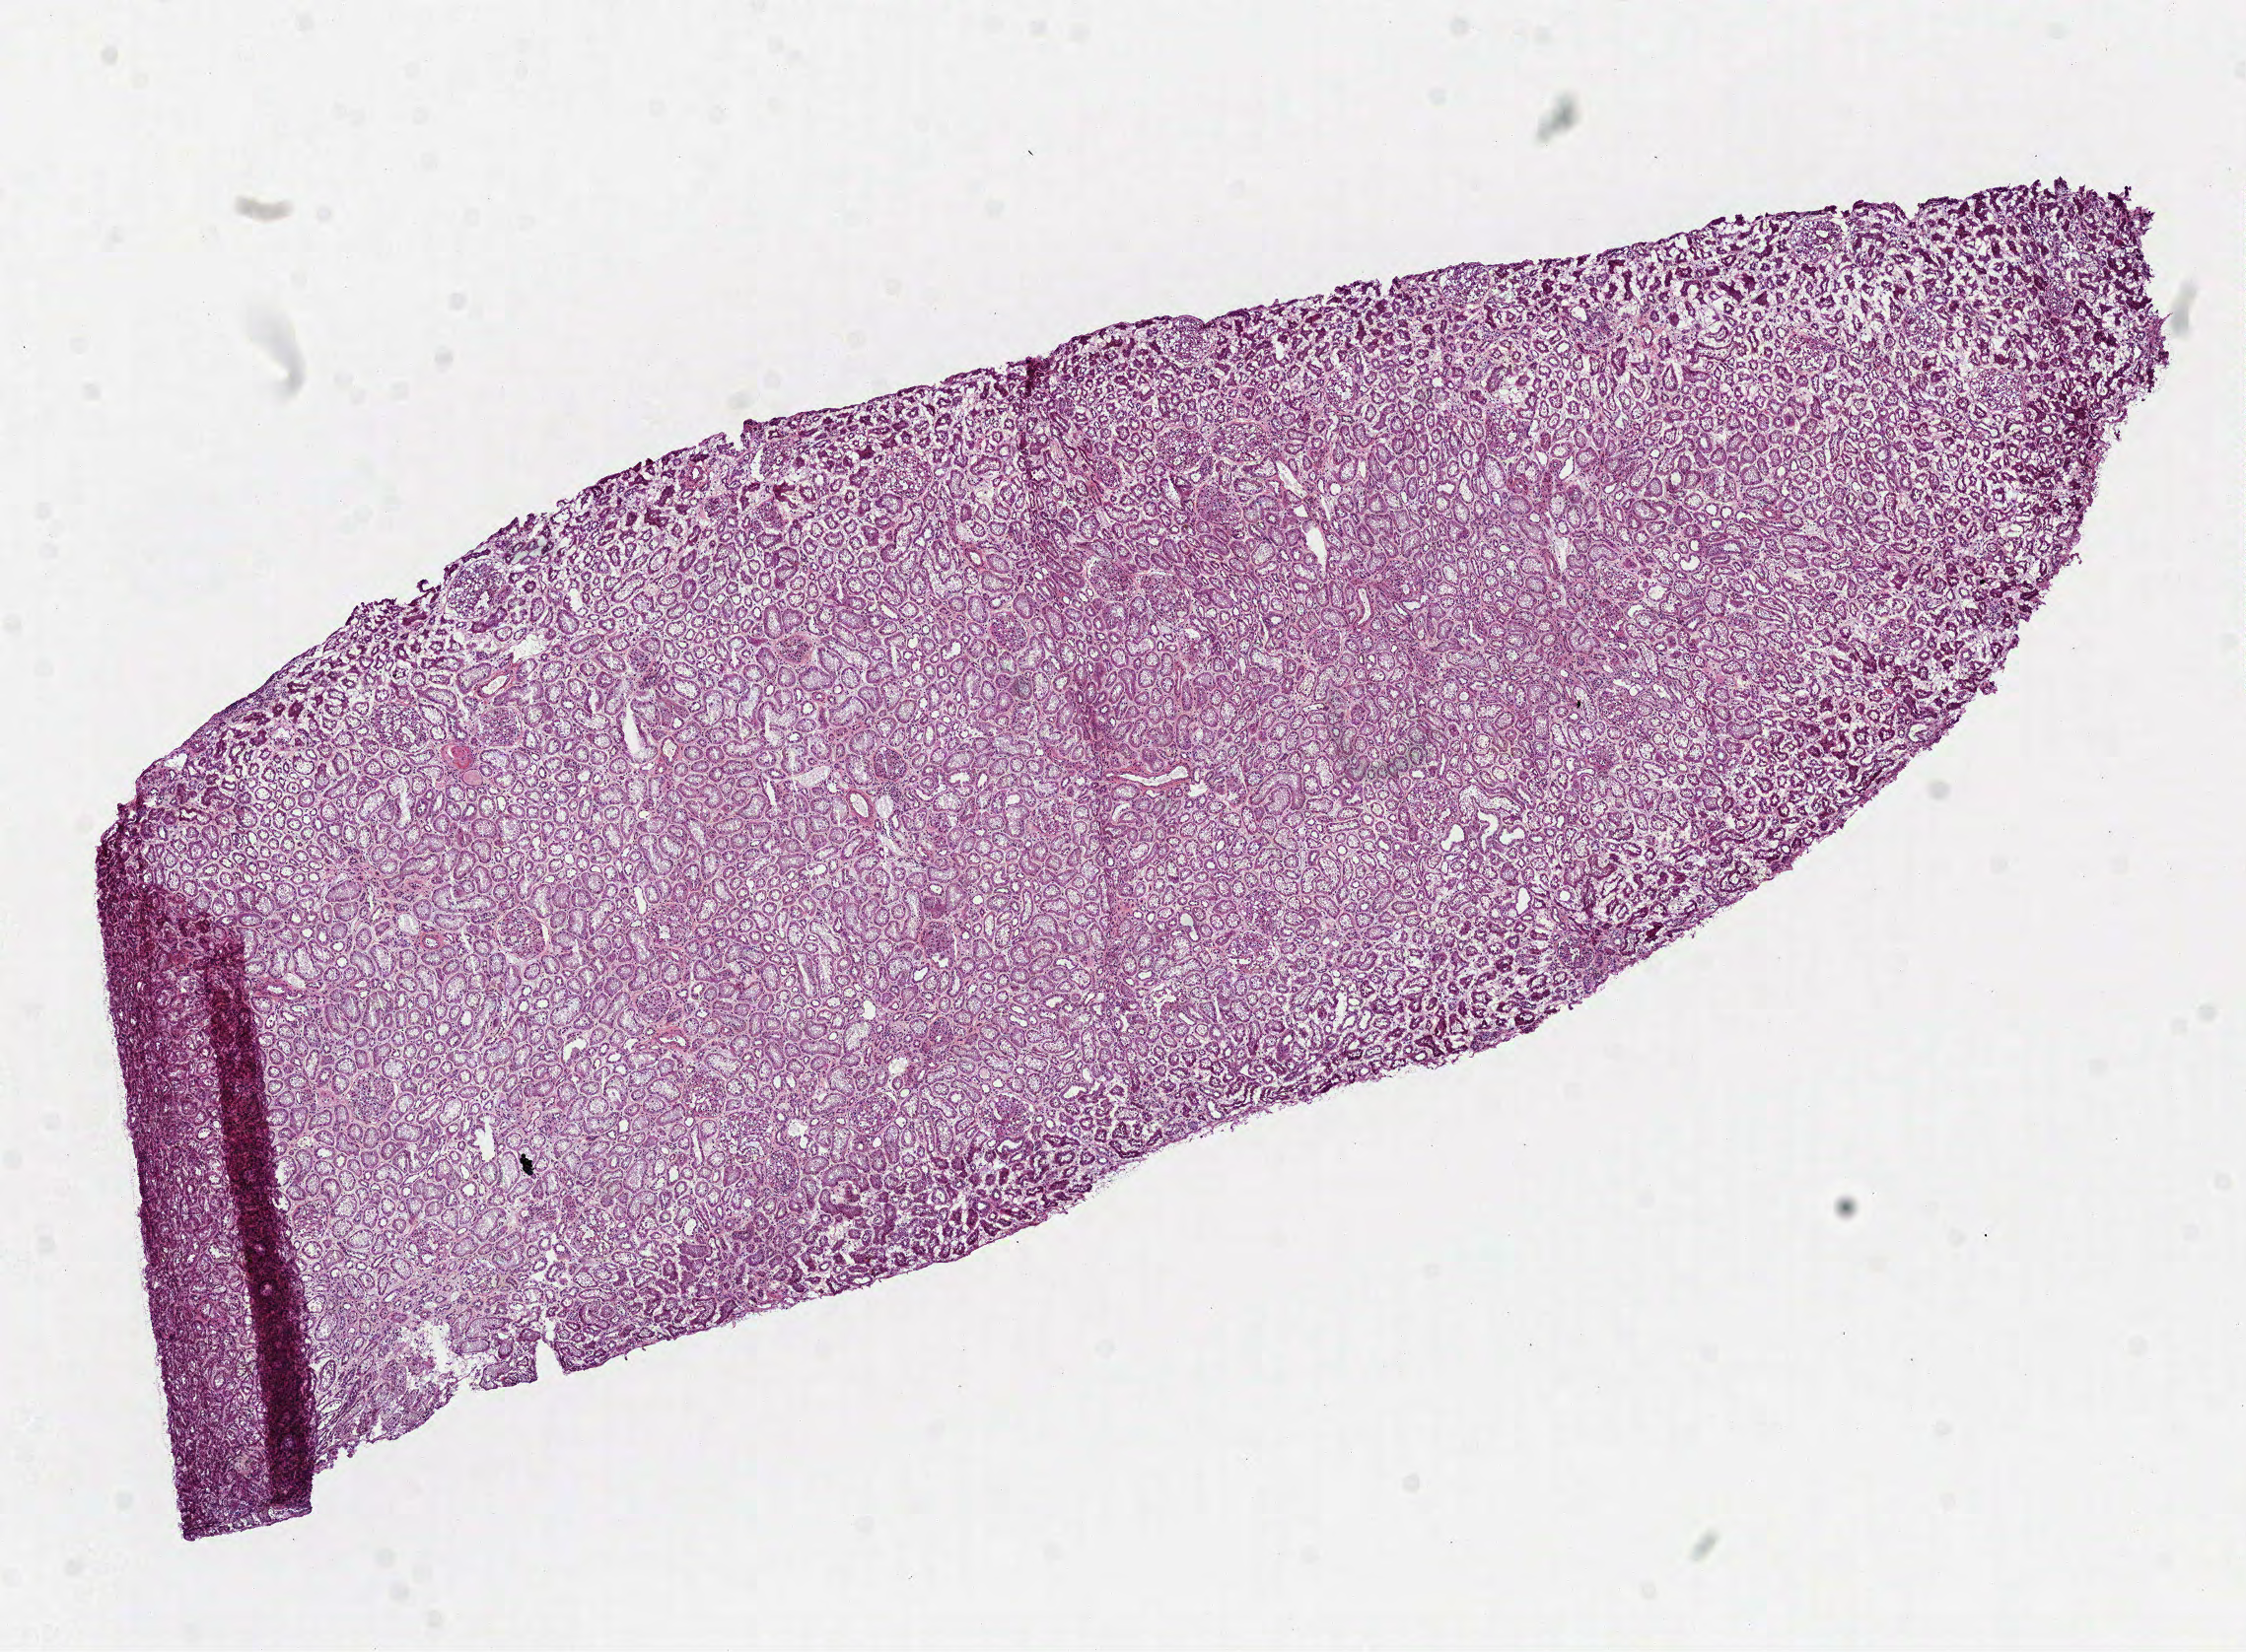
H&E whole-slide image, low-resolution overview of the scanned area, about 9.2 x 6.8 mm; frozen section from the top of the tissue portion; sample: solid tissue normal (non-tumour tissue), kidney. Female, age 38 years at initial diagnosis.
This section: solid tissue normal sample (biorepository sample class). Patient diagnosis: Clear cell adenocarcinoma, NOS.